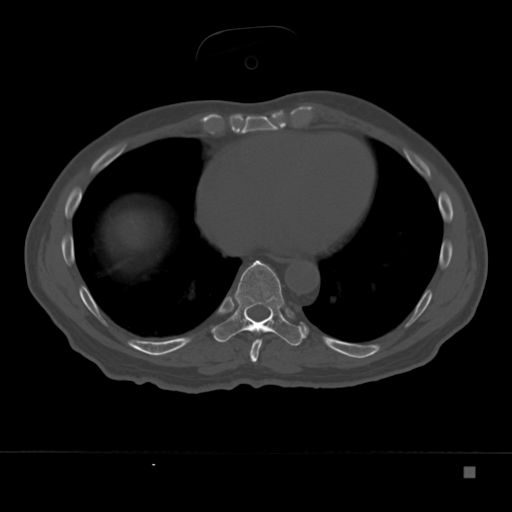
CT including the spine, one axial slice. Position 193 of 332 along the scan axis. Reconstruction kernel Br40s. 120 kVp. Bone window (W 1800 / L 400 HU). 1.5 mm slice thickness. 512 × 512 image matrix. Patient: male, 72 years. Case-level facts recorded for this patient, not image findings: primary cancer: skeletal.
Outlined on this slice (semi-automatically segmented with operator editing):
- T8 vertebra: box from (x=249, y=339) to (x=262, y=362) px
- T9 vertebra: (x=214, y=260)–(x=305, y=346)